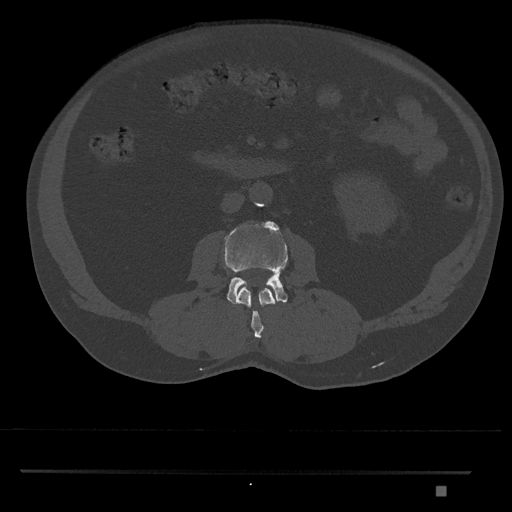
CT including the spine, one axial slice; reconstruction kernel Br40s/3; 120 kVp; bone window (W 1800 / L 400 HU); 512 × 512 image matrix, field of view 429 × 429 mm. Patient: male, 65 years. From the clinical record (not read from this slice): primary cancer: prostate.
Annotated regions visible in this slice (semi-automatic segmentation, software-assisted and operator-edited):
- L2 vertebra: box from (x=237, y=286) to (x=276, y=338) px
- L3 vertebra: (x=224, y=221)–(x=288, y=306)